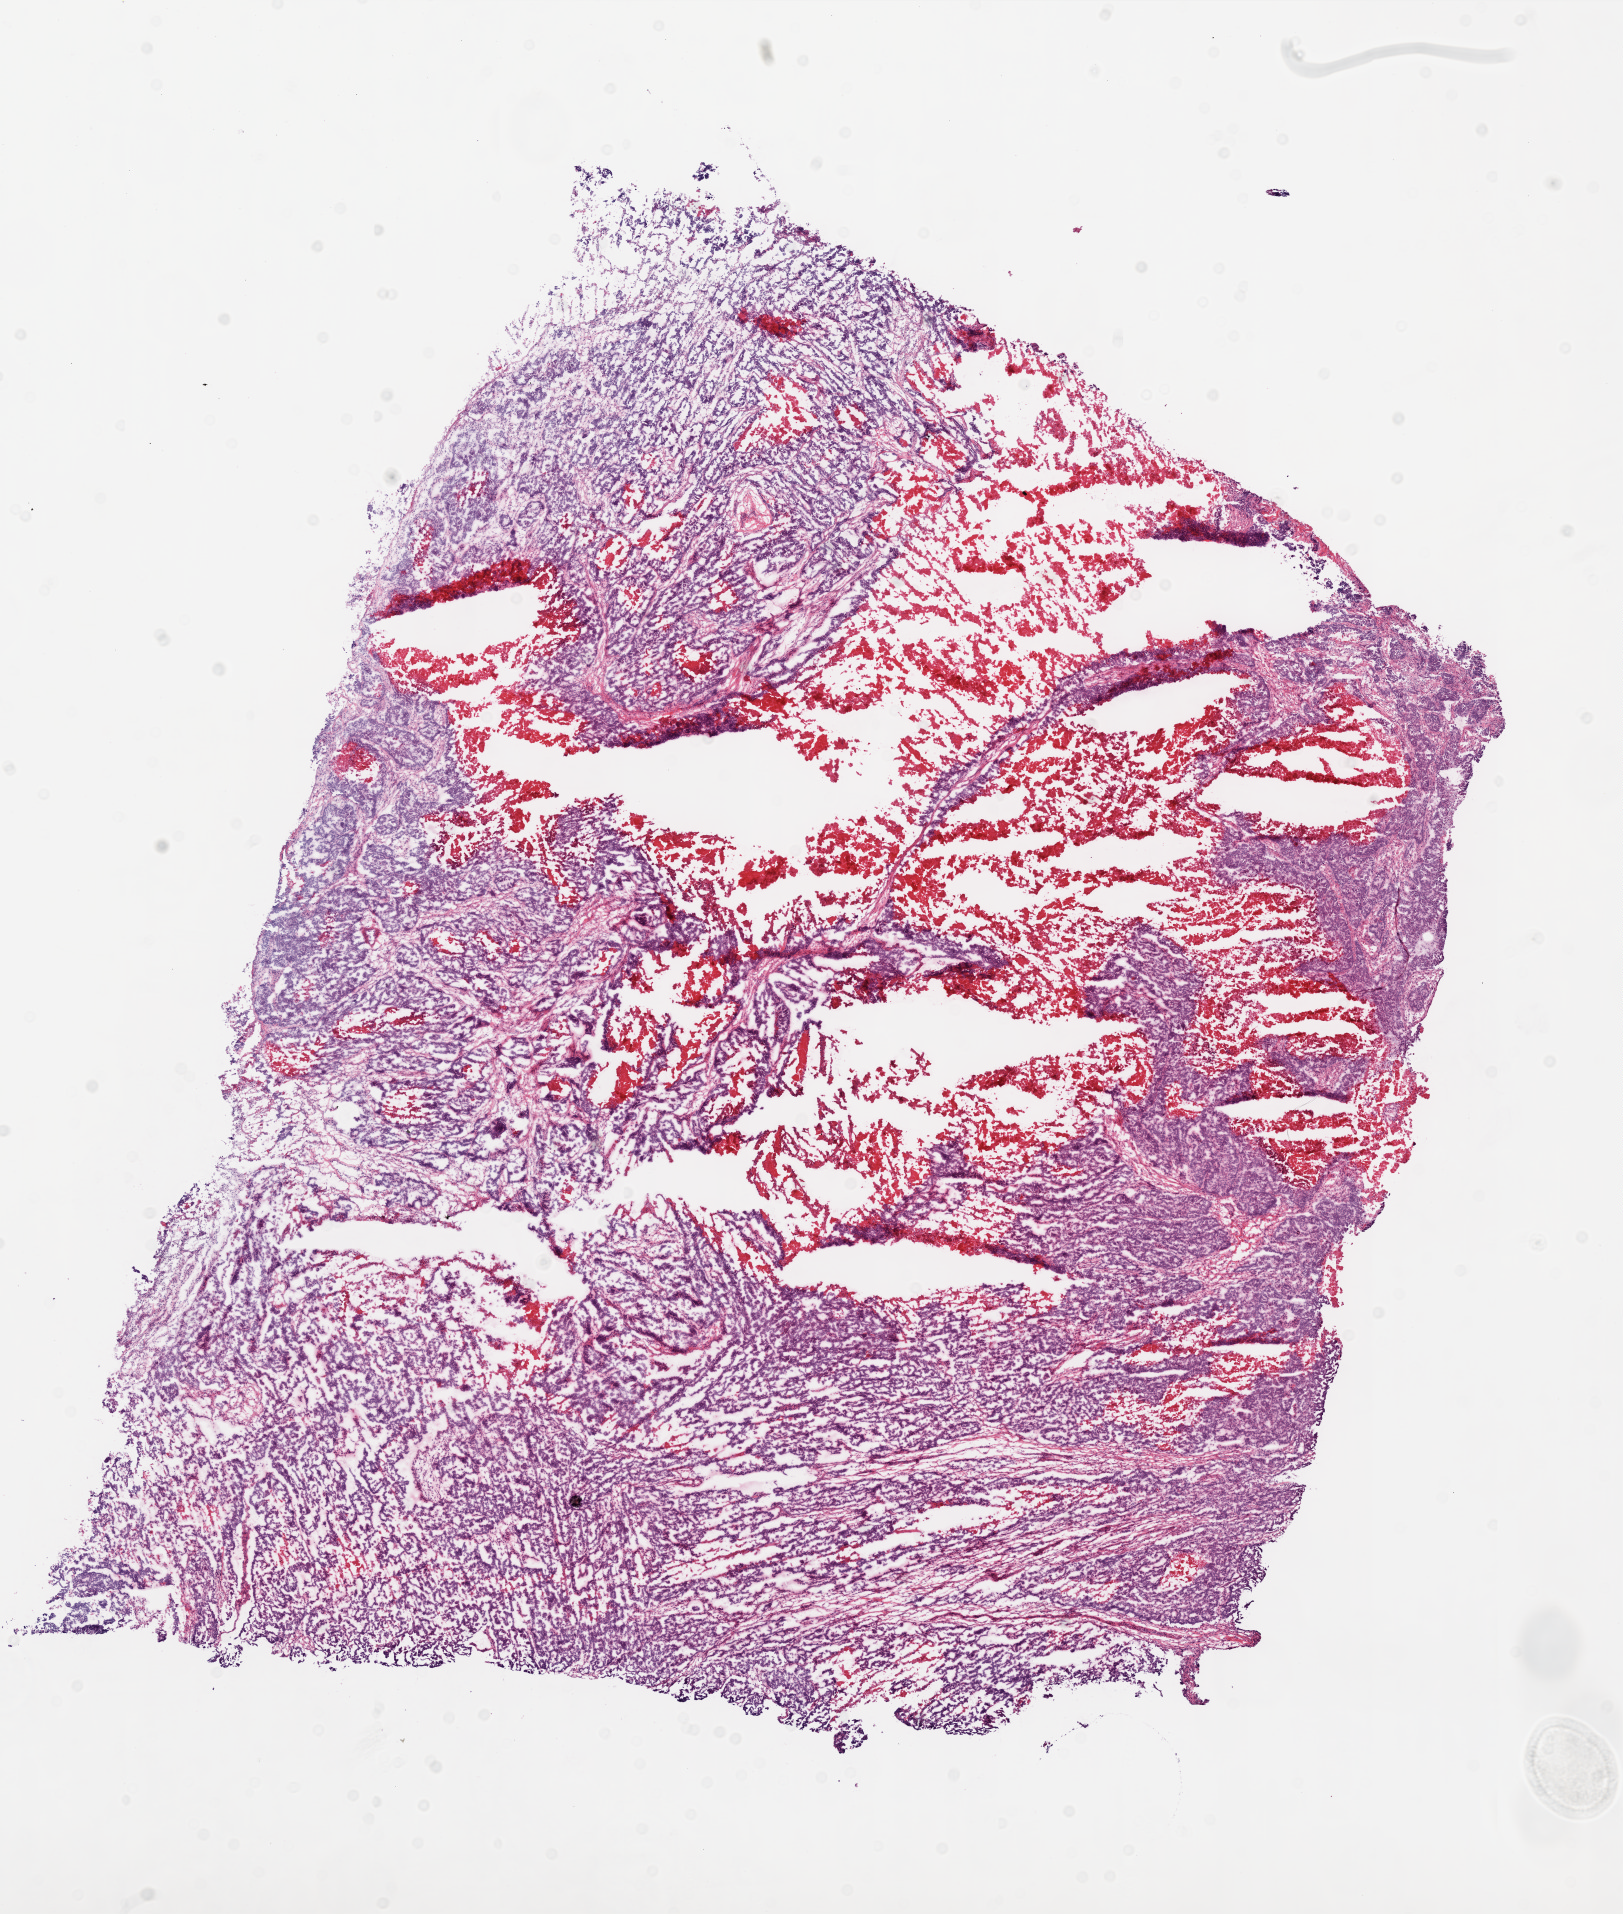
H&E-stained whole-slide image — whole scanned area (about 13.0 x 15.3 mm, acquisition: 20x scan) shown as a low-resolution overview; frozen section; sample: primary tumour, ovary. Patient: female, age at initial diagnosis 42 years. Histologic grade: G3 (poorly differentiated). Slide review estimates, as recorded: tumour cells 75%, tumour nuclei 90%, normal cells 10%, stromal cells 0%, necrosis 15%.
Pathologic diagnosis: Serous cystadenocarcinoma, NOS. FIGO stage: IV.